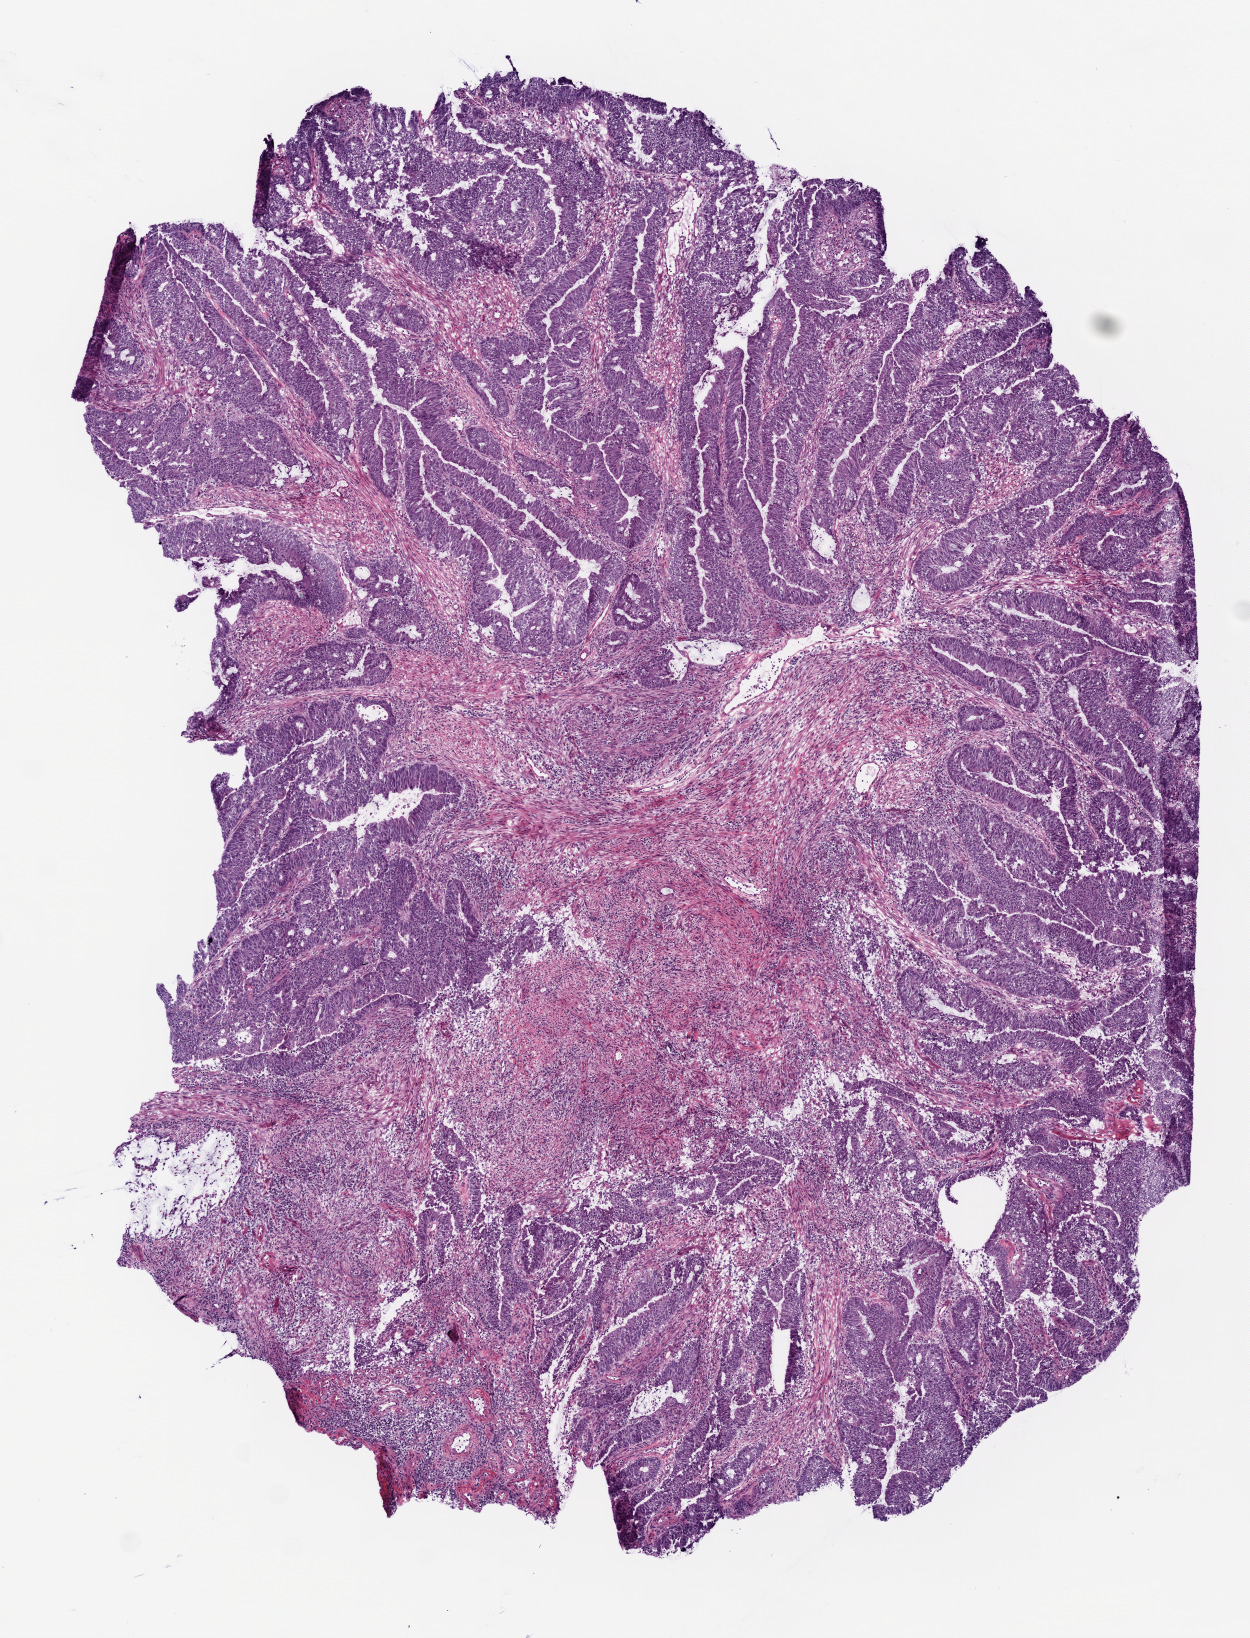
Whole-slide histology image, Hematoxylin and eosin (H&E) stained — shown as a low-resolution overview of the whole scanned area (about 5.0 x 6.6 mm); frozen section from the bottom of the tissue portion; sample: primary tumour, colon. Male patient; age at initial diagnosis 65 years. Composition of this section per pathologist review: tumour cells 70%, tumour nuclei 80%, normal cells 0%, stromal cells 30%, necrosis 0%. Infiltration values recorded for this section: lymphocyte infiltration 3%.
Lymph nodes positive (case pathology): 0 of 15 examined. Diagnosis: Adenocarcinoma, NOS (sigmoid colon).